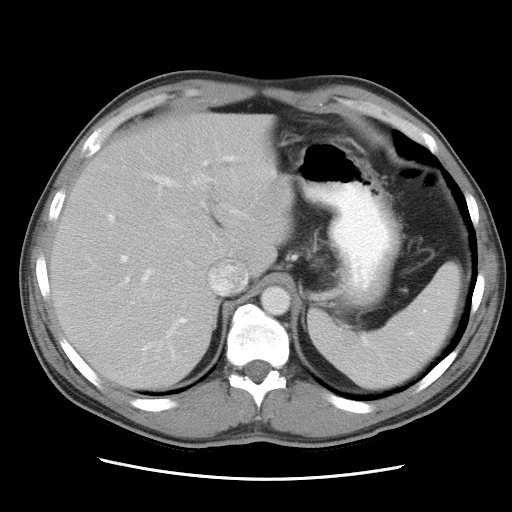
Contrast-enhanced abdominal CT, one axial slice; intravenous contrast given; soft-tissue window (W 400 / L 40 HU); 512 × 512 image matrix, field of view 360 × 360 mm. Male patient, age 40 years. From the clinical record (not read from this slice): diagnosis: colorectal cancer liver metastases, imaged before liver resection; multiple liver metastases: yes; largest metastasis: 1.5 cm.
Structures marked on this image (outlined manually by an expert reader):
- hepatic veins: bounding box <147,265,247,300> (left, top, right, bottom; pixels)
- liver: <52,115,293,387>
- planned liver remnant (the part of the liver to remain after resection): <52,114,292,388>
- portal vein (with intrahepatic branches): <108,158,240,337>